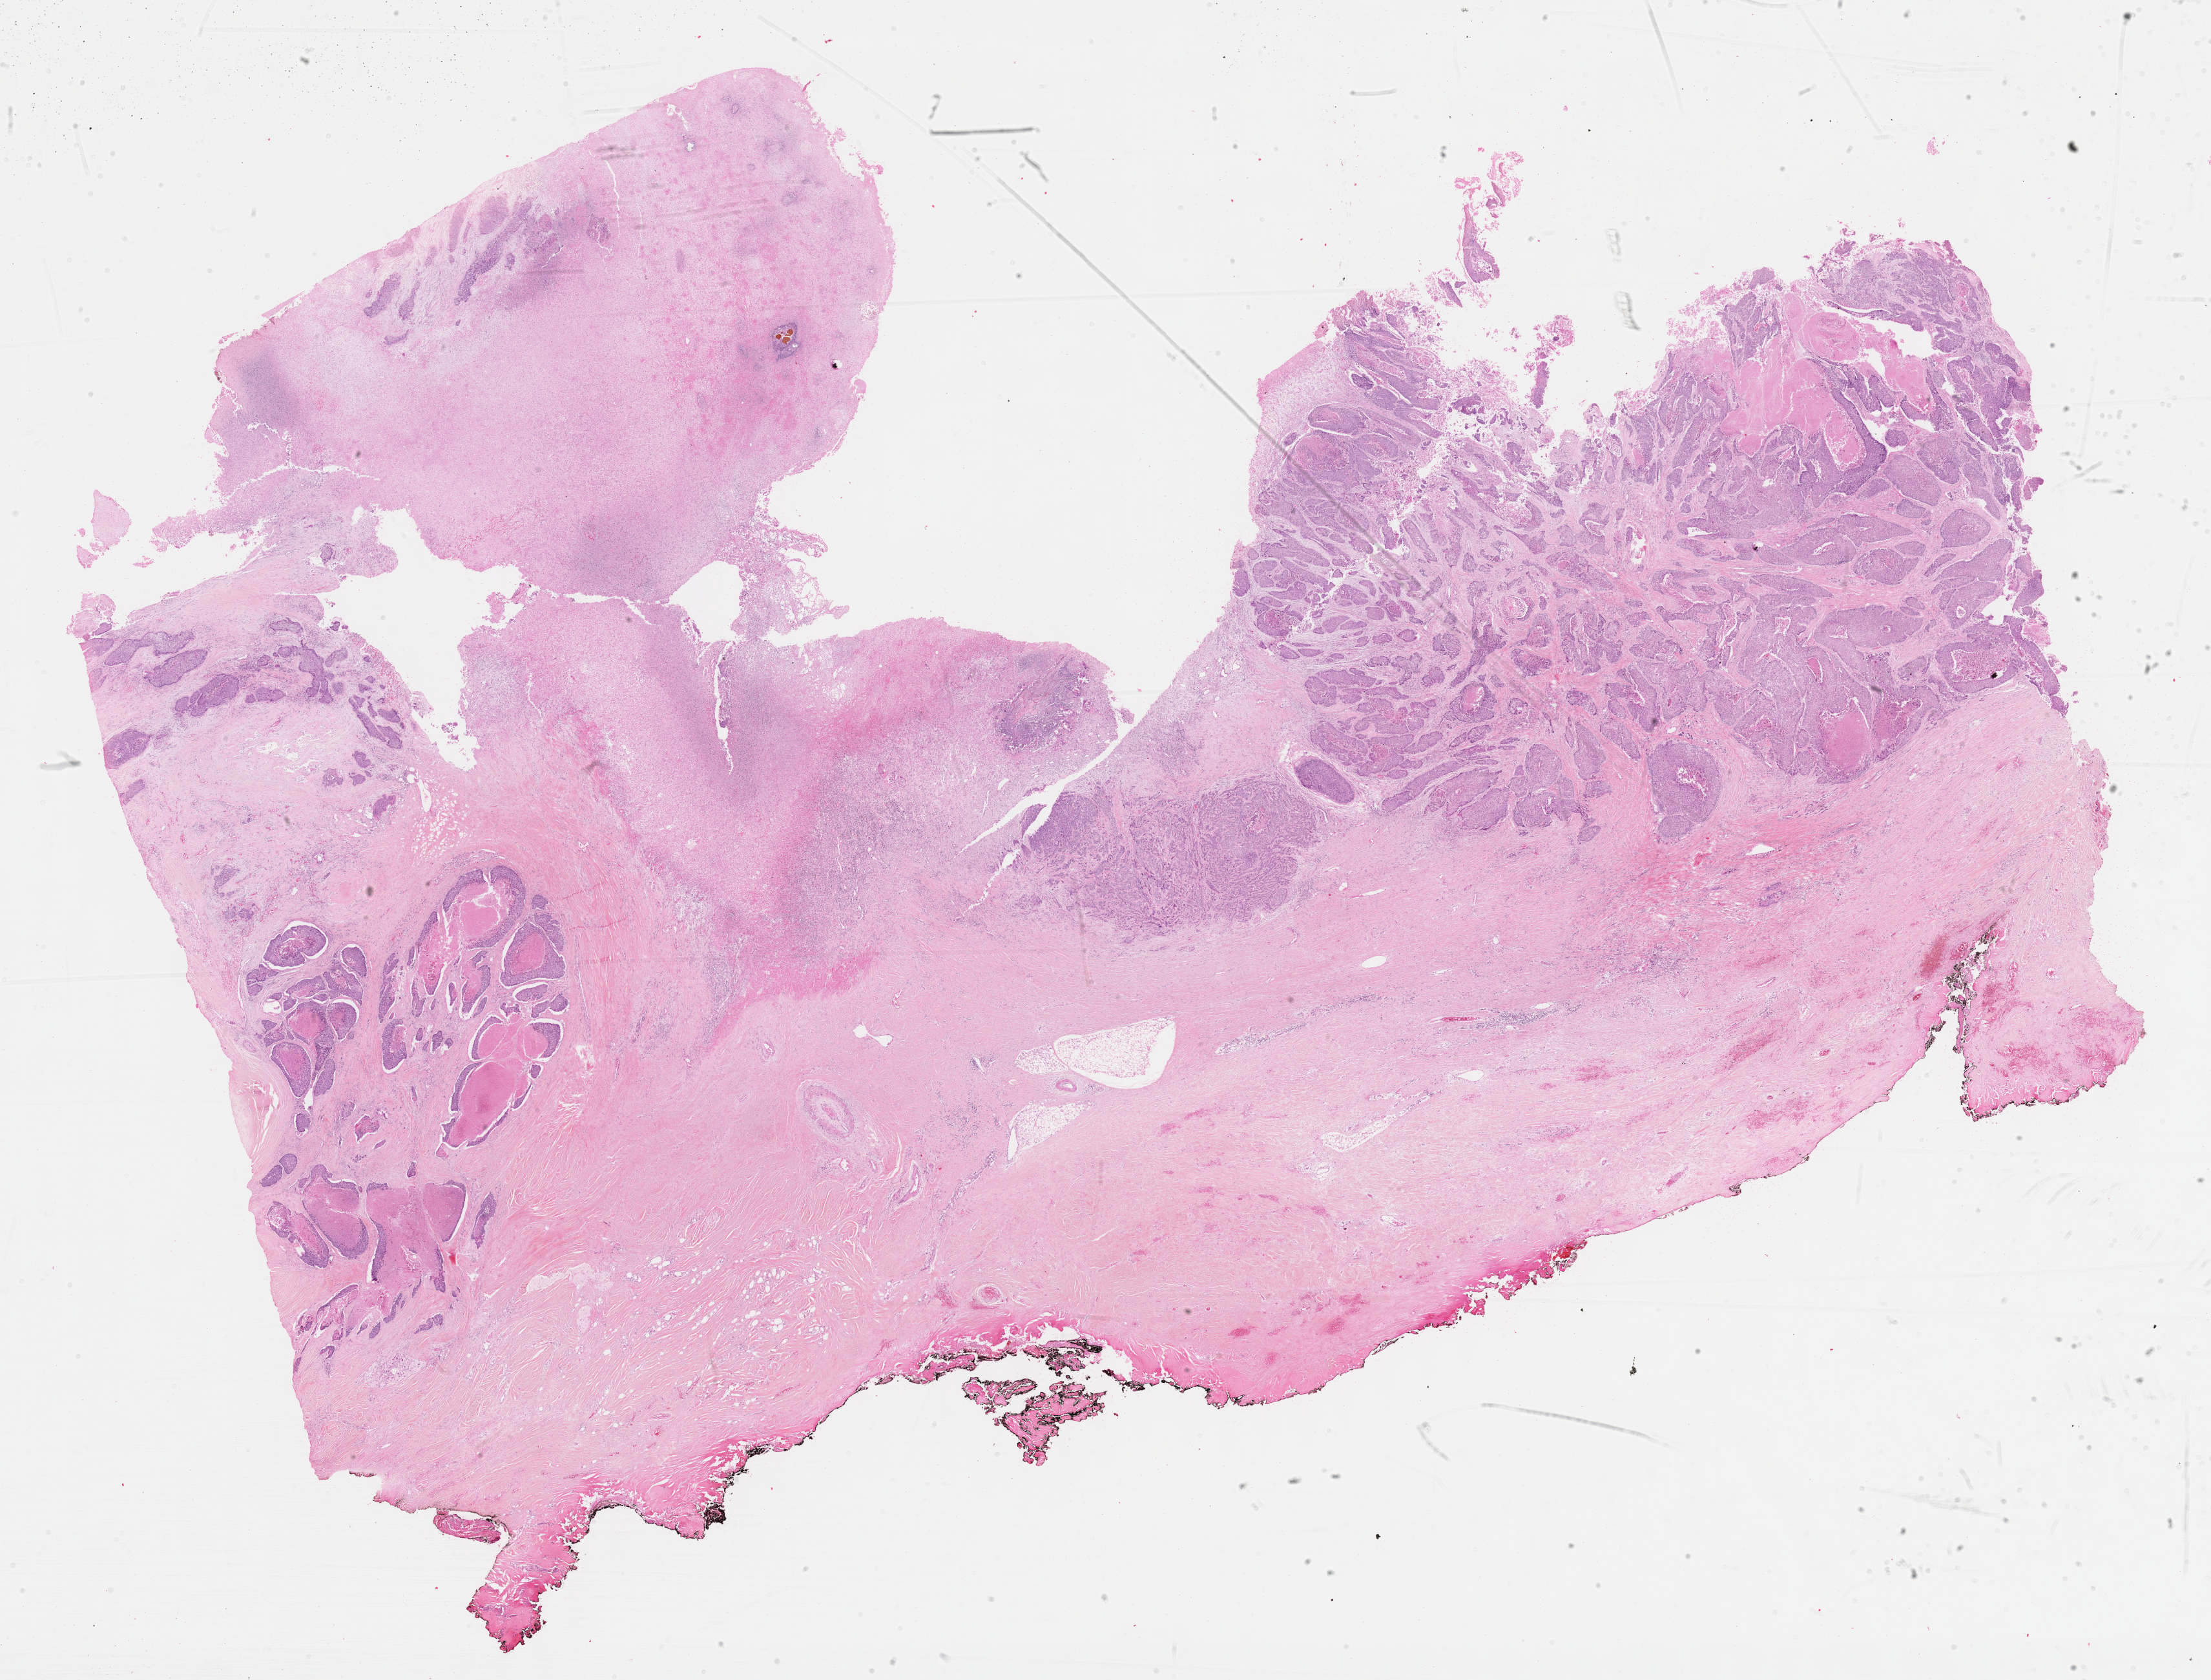
Digitized H&E tissue section (whole slide), whole scanned area (about 27.7 x 21.0 mm) shown as a low-resolution overview, FFPE section, head and neck, primary tumour sample. Male, age 65 years at initial diagnosis. Histologic grade: G2 (moderately differentiated).
AJCC pathologic stage: IVA (7th edition). Pathologic diagnosis: Squamous cell carcinoma, NOS (larynx, NOS).